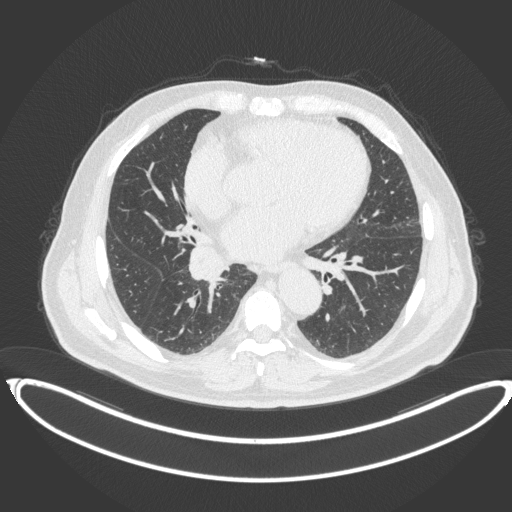
Chest CT, one axial slice; lung window (W 1500 / L -600 HU); 1 mm slice thickness; 512 × 512 image matrix, field of view 448 × 448 mm. Male patient, age 61 years. Case-level facts recorded for this patient, not image findings: clinical TNM (as recorded): T1b N1 M0.
Structures marked on this image (rectangle marked by the reading radiologist):
- lung tumour (recorded histology: squamous cell carcinoma): box from (x=184, y=242) to (x=229, y=284) px